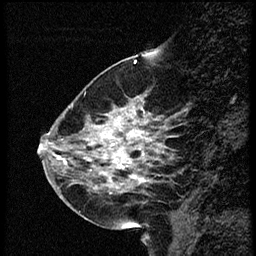
Breast MRI (dynamic contrast-enhanced), one sagittal slice. Slice 17 of 56 in the series (ordered by position). Dynamic contrast-enhanced study with each time point stored as its own series, time point 2 of 4 at this slice position (early post-contrast, ordered by acquisition time). 1.5 T. TE 4.2 ms, TR 18.9 ms. 2 mm slice thickness. 256 × 256 image matrix, field of view 200 × 200 mm. Female patient. Case-level facts recorded for this patient, not image findings: setting: breast cancer imaged before/during neoadjuvant chemotherapy; receptor status: HER2-positive.
Annotated regions visible in this slice (semi-automatic segmentation, software-assisted and operator-edited):
- analysis volume of interest (the breast-tissue region the enhancement analysis was run in; not a lesion): box from (x=63, y=80) to (x=169, y=215) px
- tumour enhancement mask (voxels above the 100 % enhancement threshold inside the analysis volume of interest): (x=92, y=96)–(x=155, y=187)